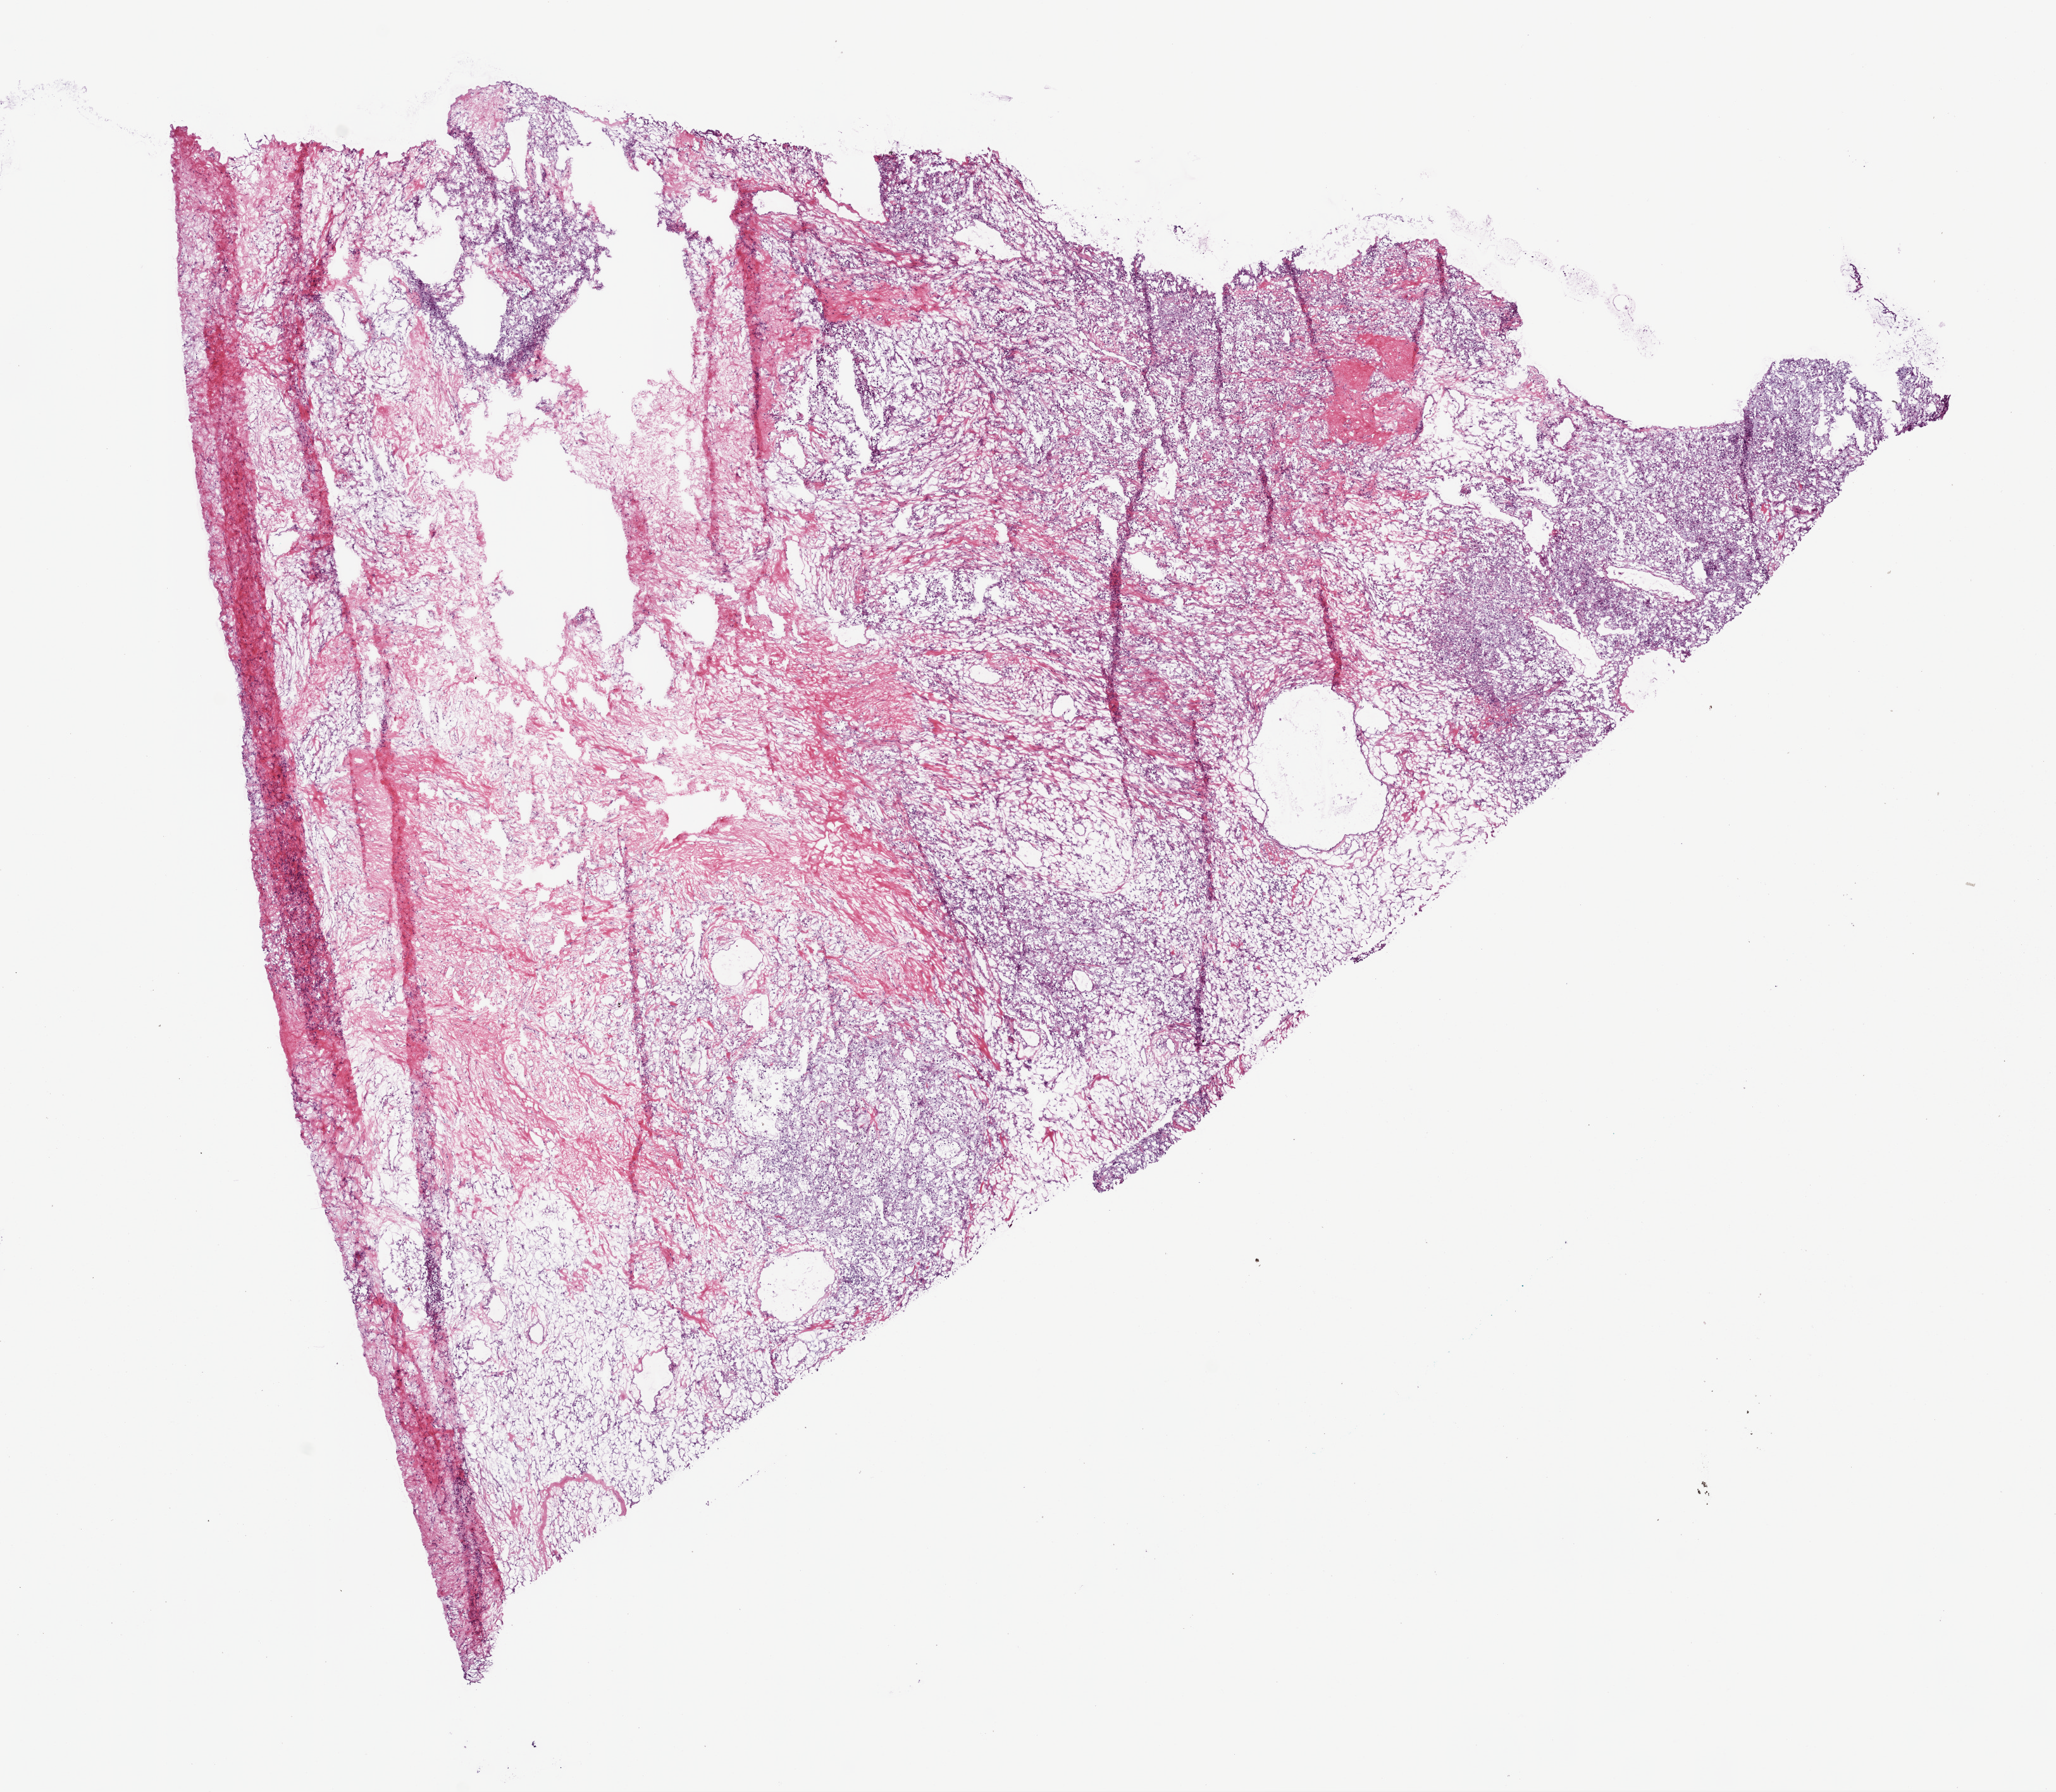
Digitized Hematoxylin and eosin (H&E) stained tissue section (whole slide) — a low-resolution overview of the entire scanned area, about 13.0 x 11.4 mm (slide scanned at 20x); frozen section from the top of the tissue portion; sample: primary tumour, kidney. Patient: male, age at initial diagnosis 63 years. Histologic grade: G3 (poorly differentiated). Pathologist review of this section (percent, as recorded): tumour cells 50%, tumour nuclei 70%, normal cells 0%, stromal cells 50%, necrosis 0%.
Laterality: right. Histologic diagnosis: Clear cell adenocarcinoma, NOS. AJCC pathologic stage: IV.